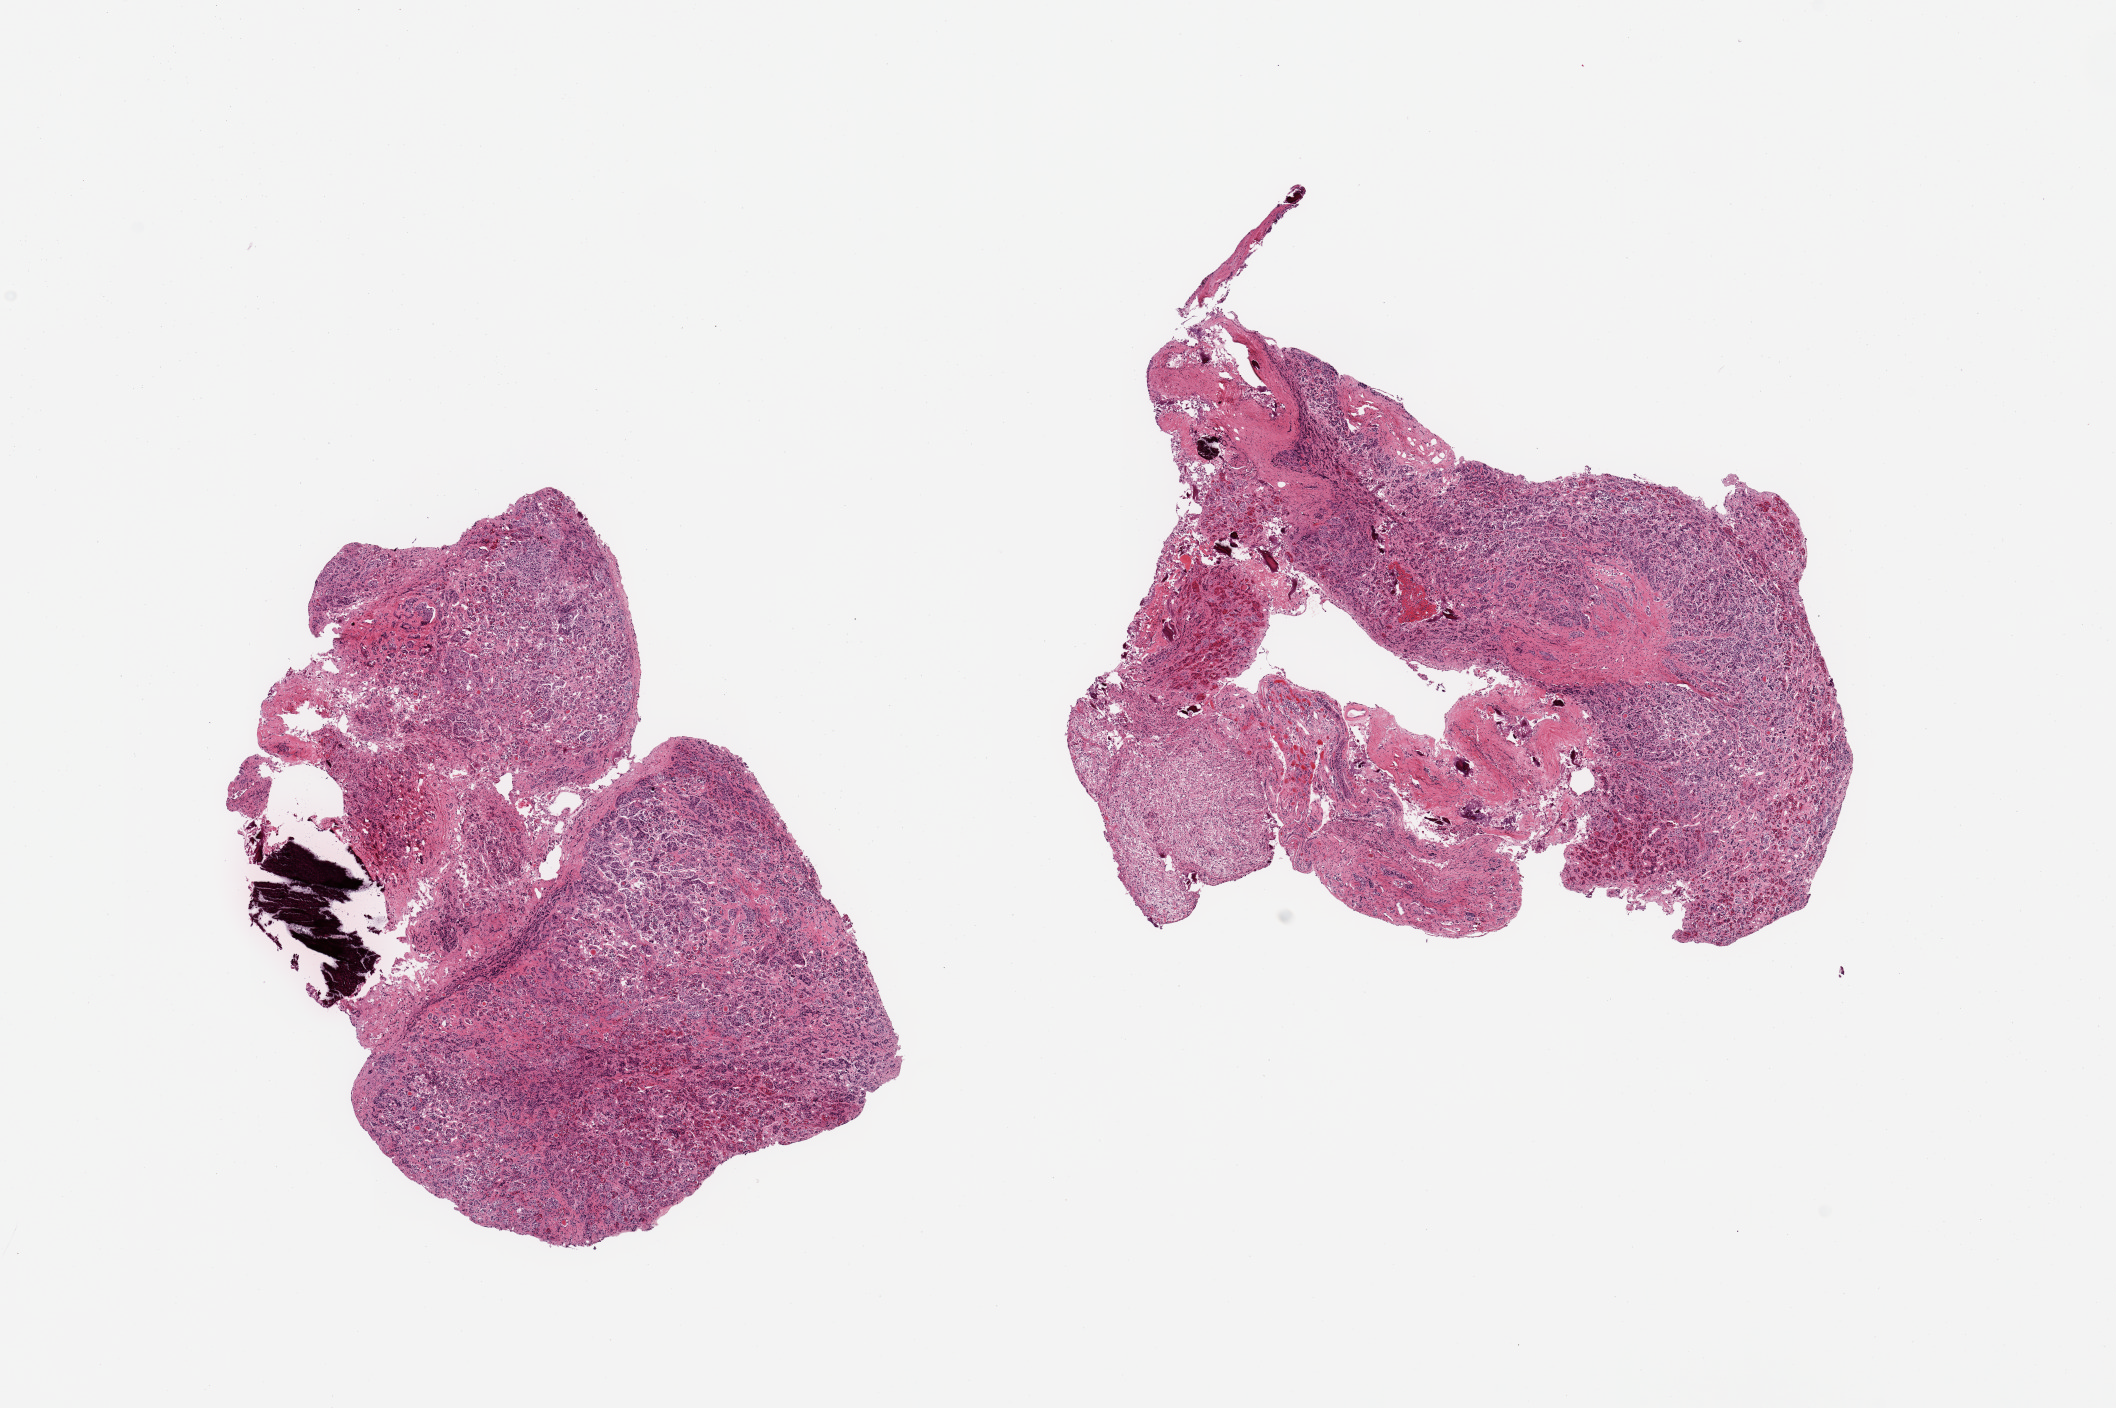
Haematoxylin and eosin whole-slide image — whole scanned area (about 16.7 x 11.1 mm, slide scanned at 20x) shown as a low-resolution overview. PAXgene-fixed, paraffin-embedded tissue. Section of pituitary (target tissue). Donor tissue sample. Donor: male.
Pathologist's review note for this sample: 2 pieces; mostly adenohypophysis and neurohypophysis; disseminated calcifications.